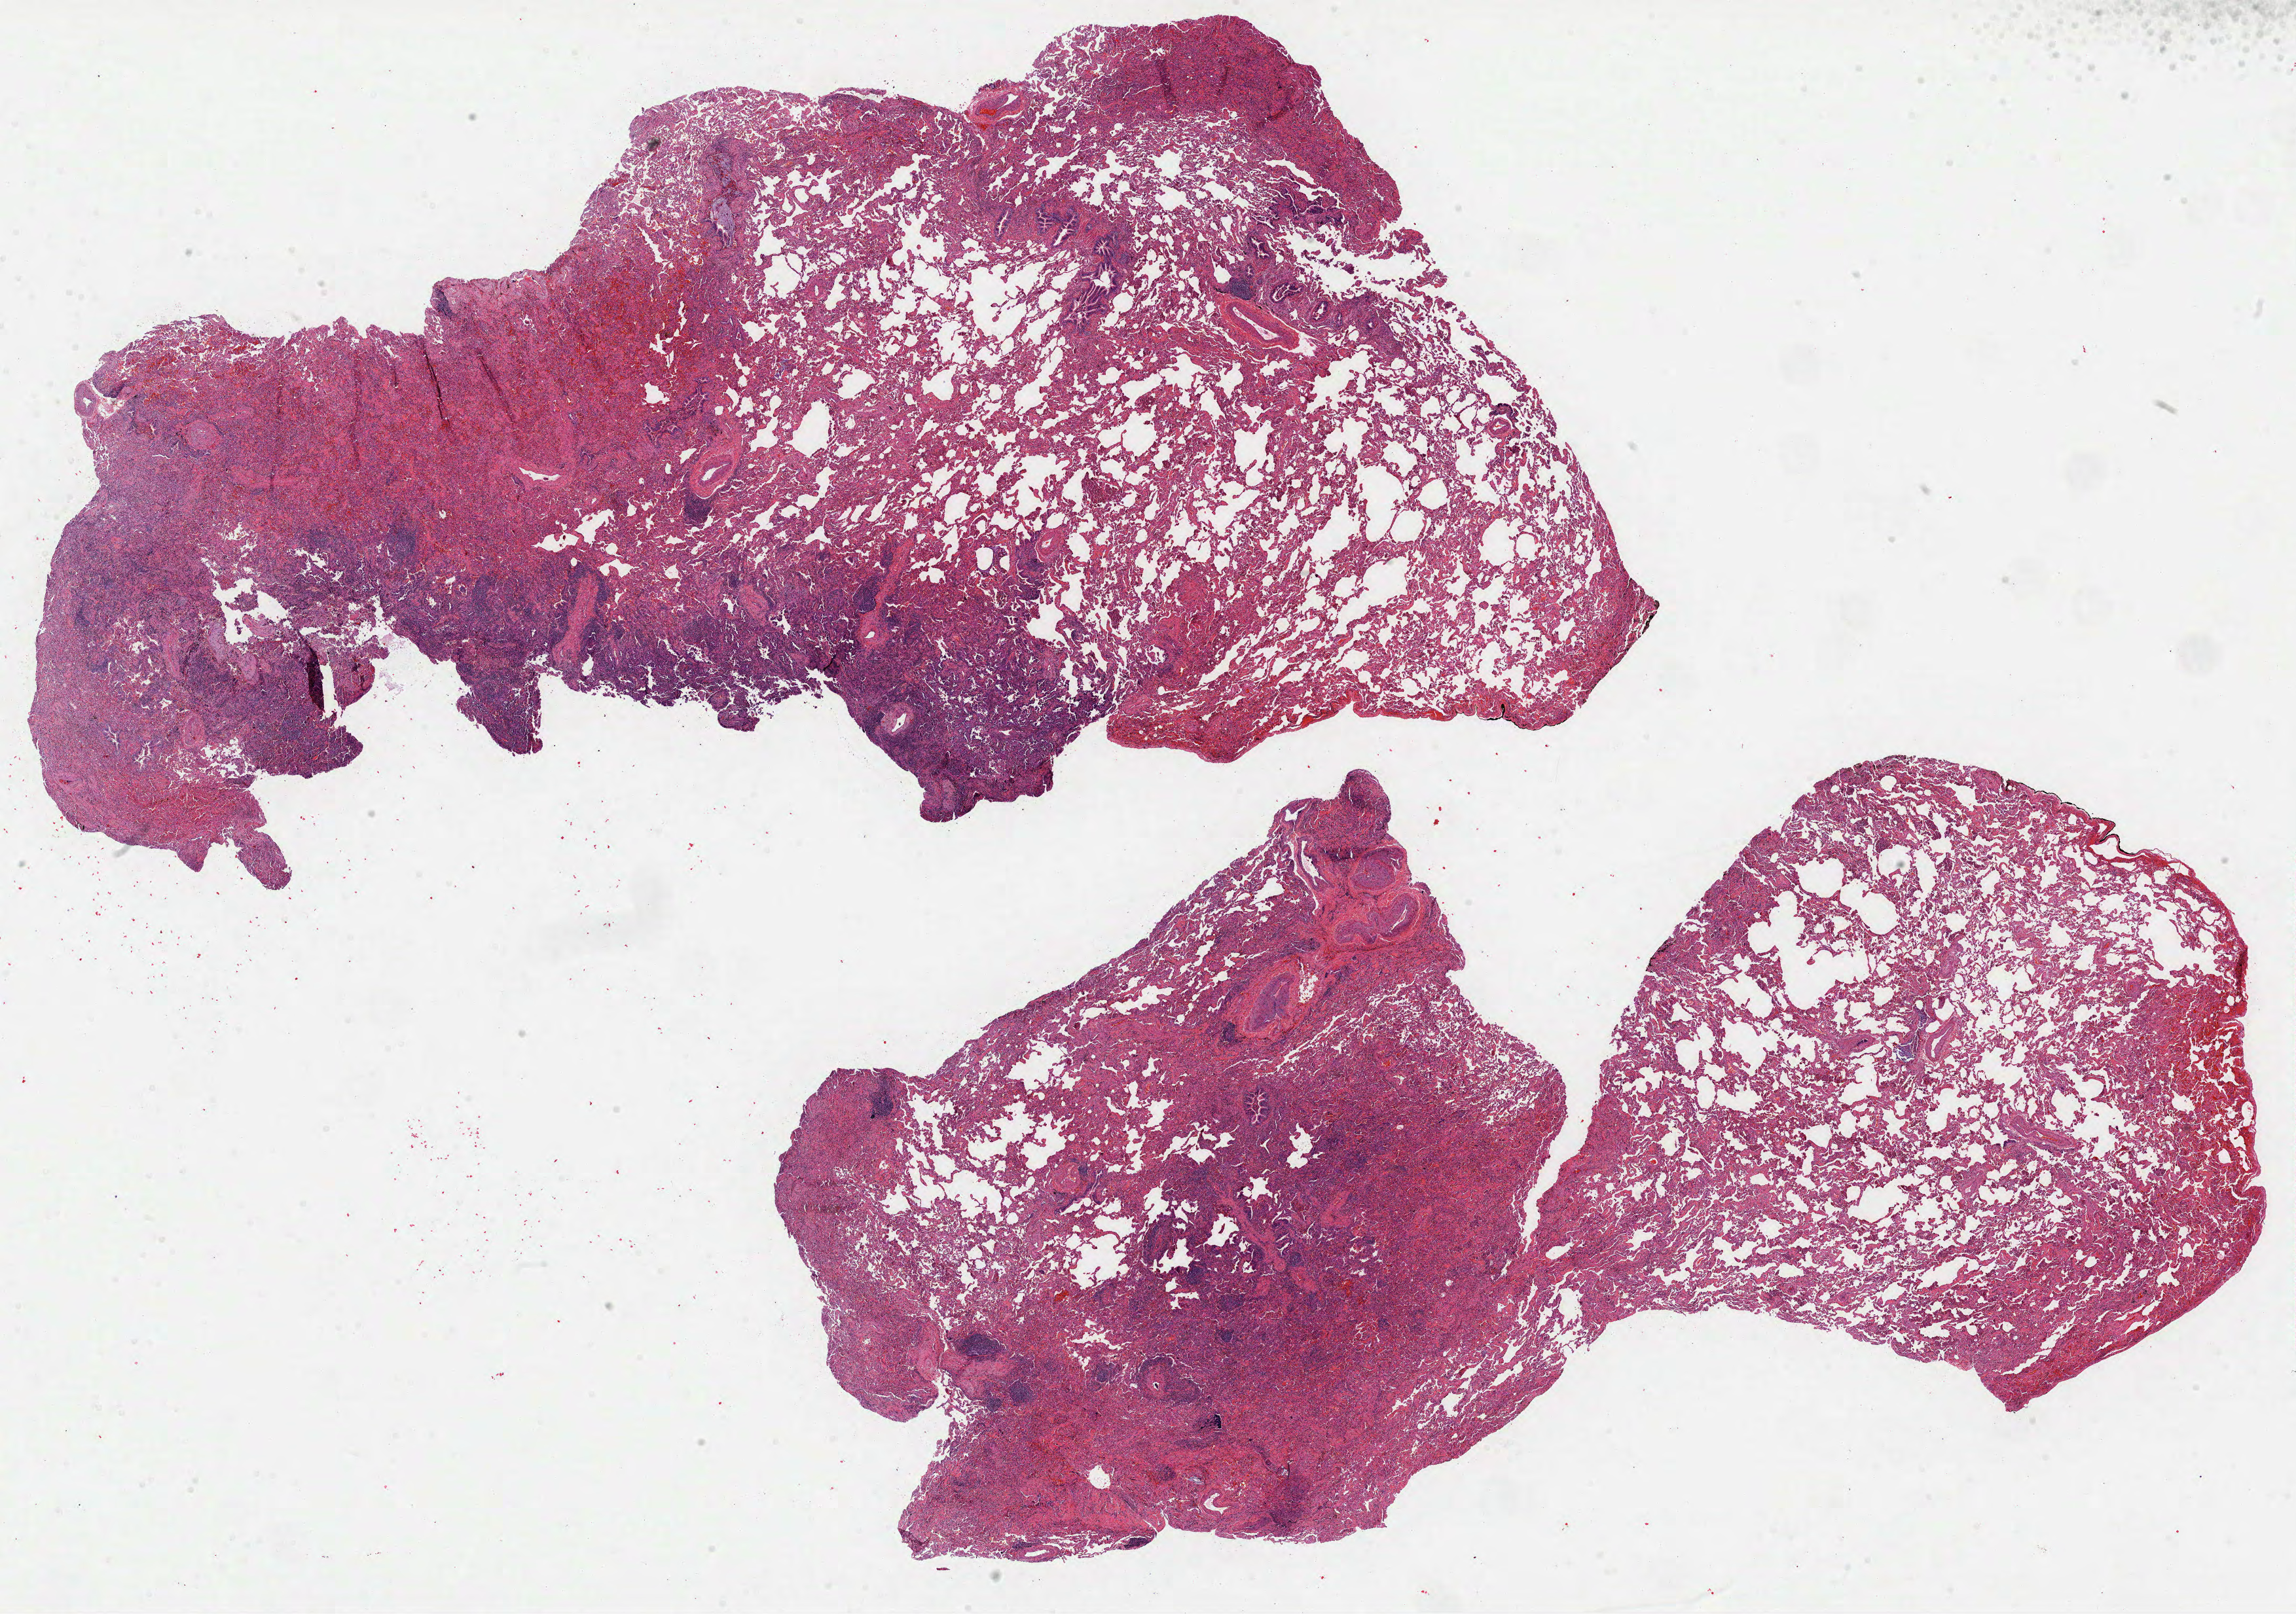
Hematoxylin and eosin (H&E) stained whole-slide image, whole scanned area (about 28.3 x 19.9 mm) shown as a low-resolution overview. Formalin-fixed paraffin-embedded (FFPE) diagnostic section. Lung, primary tumour sample. Female patient; age at initial diagnosis 58 years.
TNM: T1 N0 MX. AJCC pathologic stage: IA. Laterality: left. Diagnosis: Bronchiolo-alveolar carcinoma, non-mucinous (lower lobe, lung).